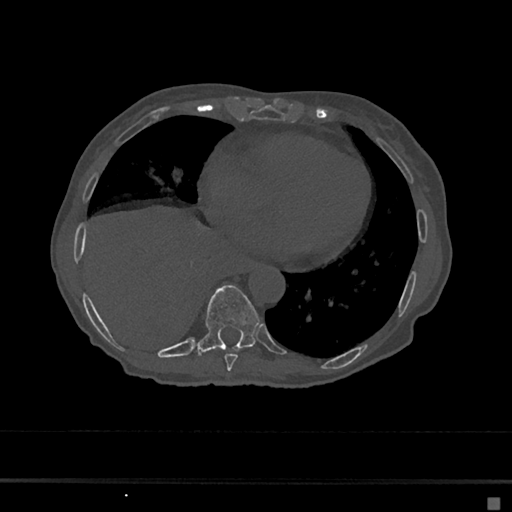
CT including the spine, one axial slice. Slice 289 of 797 in the series (ordered by position). 120 kVp. Bone window (W 1800 / L 400 HU). 0.5 mm slice thickness. 512 × 512 image matrix, field of view 360 × 360 mm. Female patient, age 68 years. From the clinical record (not read from this slice): primary cancer: renal.
Annotated regions visible in this slice (semi-automatic segmentation, software-assisted and operator-edited):
- T8 vertebra: bounding box <224,354,238,371> (left, top, right, bottom; pixels)
- T9 vertebra: <197,285,260,355>